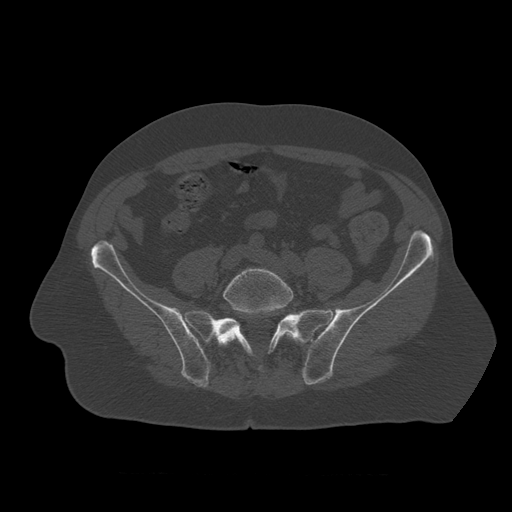
CT including the spine, one axial slice; position 245 of 450 along the scan axis; reconstruction kernel STANDARD; 120 kVp; bone window (W 1800 / L 400 HU); 1.25 mm slice thickness; 512 × 512 image matrix, field of view 405 × 405 mm. Patient age 75 years. From the clinical record (not read from this slice): primary cancer: prostate.
Outlined on this slice (semi-automatically segmented with operator editing):
- L5 vertebra: bounding box [x1, y1, x2, y2] px = [221, 268, 295, 346]